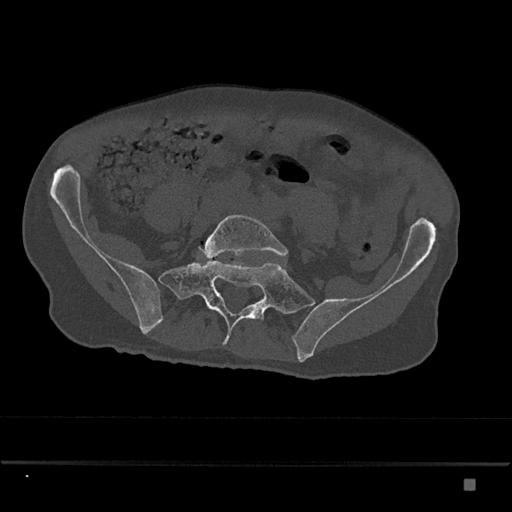
CT including the spine, one axial slice; position 239 of 797 along the scan axis; reconstruction kernel Br40s/3; bone window (W 1800 / L 400 HU); 0.5 mm slice thickness; 512 × 512 image matrix, field of view 390 × 390 mm. Patient: male, 72 years. Case-level facts recorded for this patient, not image findings: primary cancer: prostate.
Structures marked on this image (semi-automatically segmented with operator editing):
- L5 vertebra: bounding box <203,214,288,260> (left, top, right, bottom; pixels)